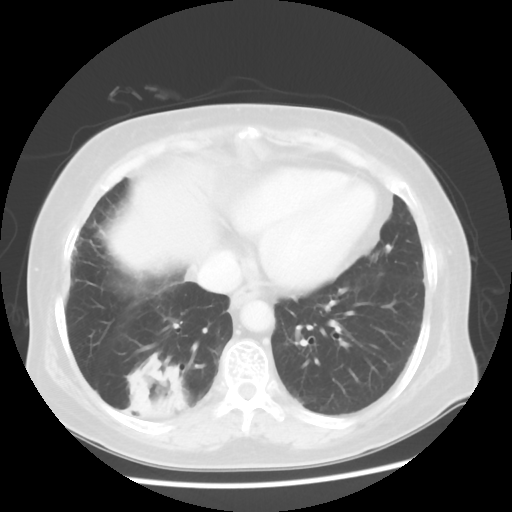
Chest CT, one axial slice. Slice 18 of 56 in the series (ordered by position). Reconstruction kernel STANDARD. 120 kVp. Lung window (W 1500 / L -600 HU). 512 × 512 image matrix. Patient: female, 64 years. From the clinical record (not read from this slice): clinical TNM (as recorded): Tis N0 M0.
Annotated regions visible in this slice (bounding box drawn by a radiologist):
- lung tumour (recorded histology: adenocarcinoma): bounding box <113,348,197,433> (left, top, right, bottom; pixels)